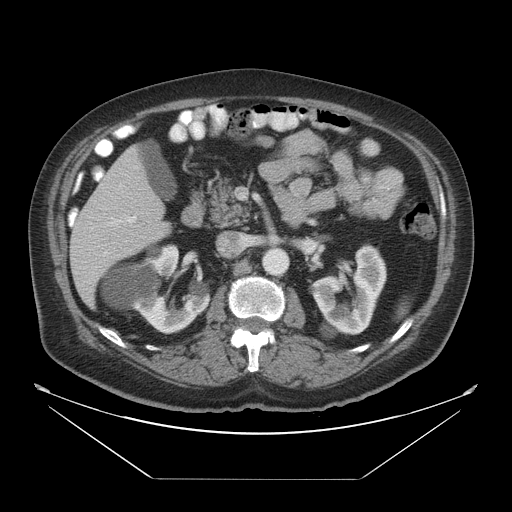
Contrast-enhanced abdominal CT, one axial slice. Slice 22 of 45 in the series (ordered by position). Reconstruction kernel STANDARD. 120 kVp. Intravenous contrast given. Soft-tissue window (W 400 / L 40 HU). 5 mm slice thickness. 512 × 512 image matrix. Male patient, age 87 years. From the clinical record (not read from this slice): diagnosis: colorectal cancer liver metastases, imaged before liver resection; multiple liver metastases: no; largest metastasis: 4.5 cm; disease in both lobes: yes.
Structures marked on this image (outlined manually by an expert reader):
- liver: bounding box <70,145,172,308> (left, top, right, bottom; pixels)
- portal vein (with intrahepatic branches): <120,184,136,223>